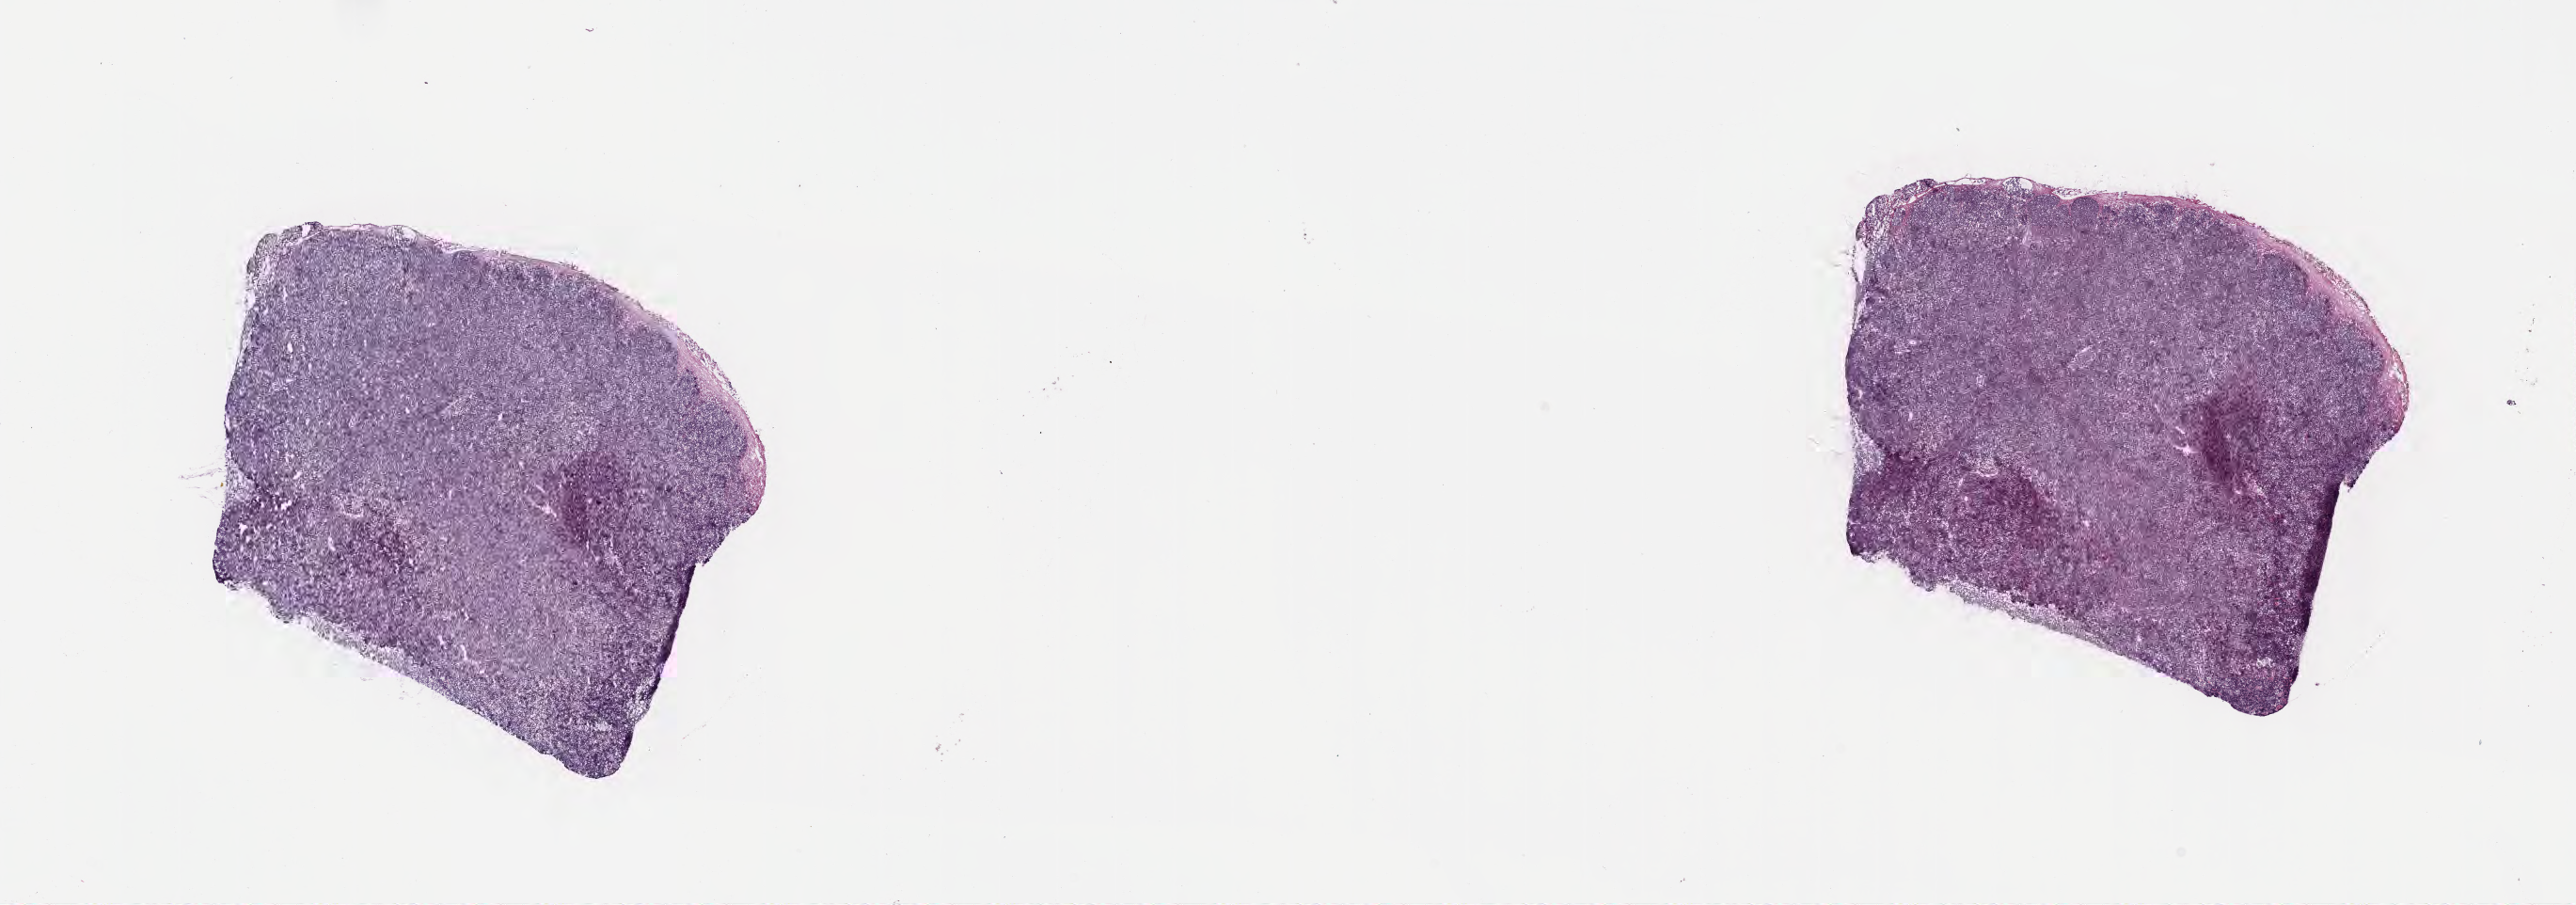
Whole-slide image, haematoxylin and eosin stain — shown as a low-resolution overview of the whole scanned area (about 22.1 x 7.8 mm), cryosection, primary tumor, anatomic site: cranium. Male patient; age at initial diagnosis 8 years. Slide review estimates, as recorded: tumor cells 85%, tumor nuclei 85%, stromal cells 10%, necrosis 5%, normal cells 0%. Infiltration values recorded for this section: lymphocyte infiltration 50%, monocyte infiltration 30%, neutrophil infiltration 5%.
Ann Arbor stage (patient): Stage I. Diagnosis: Diffuse large B-cell lymphoma, NOS.